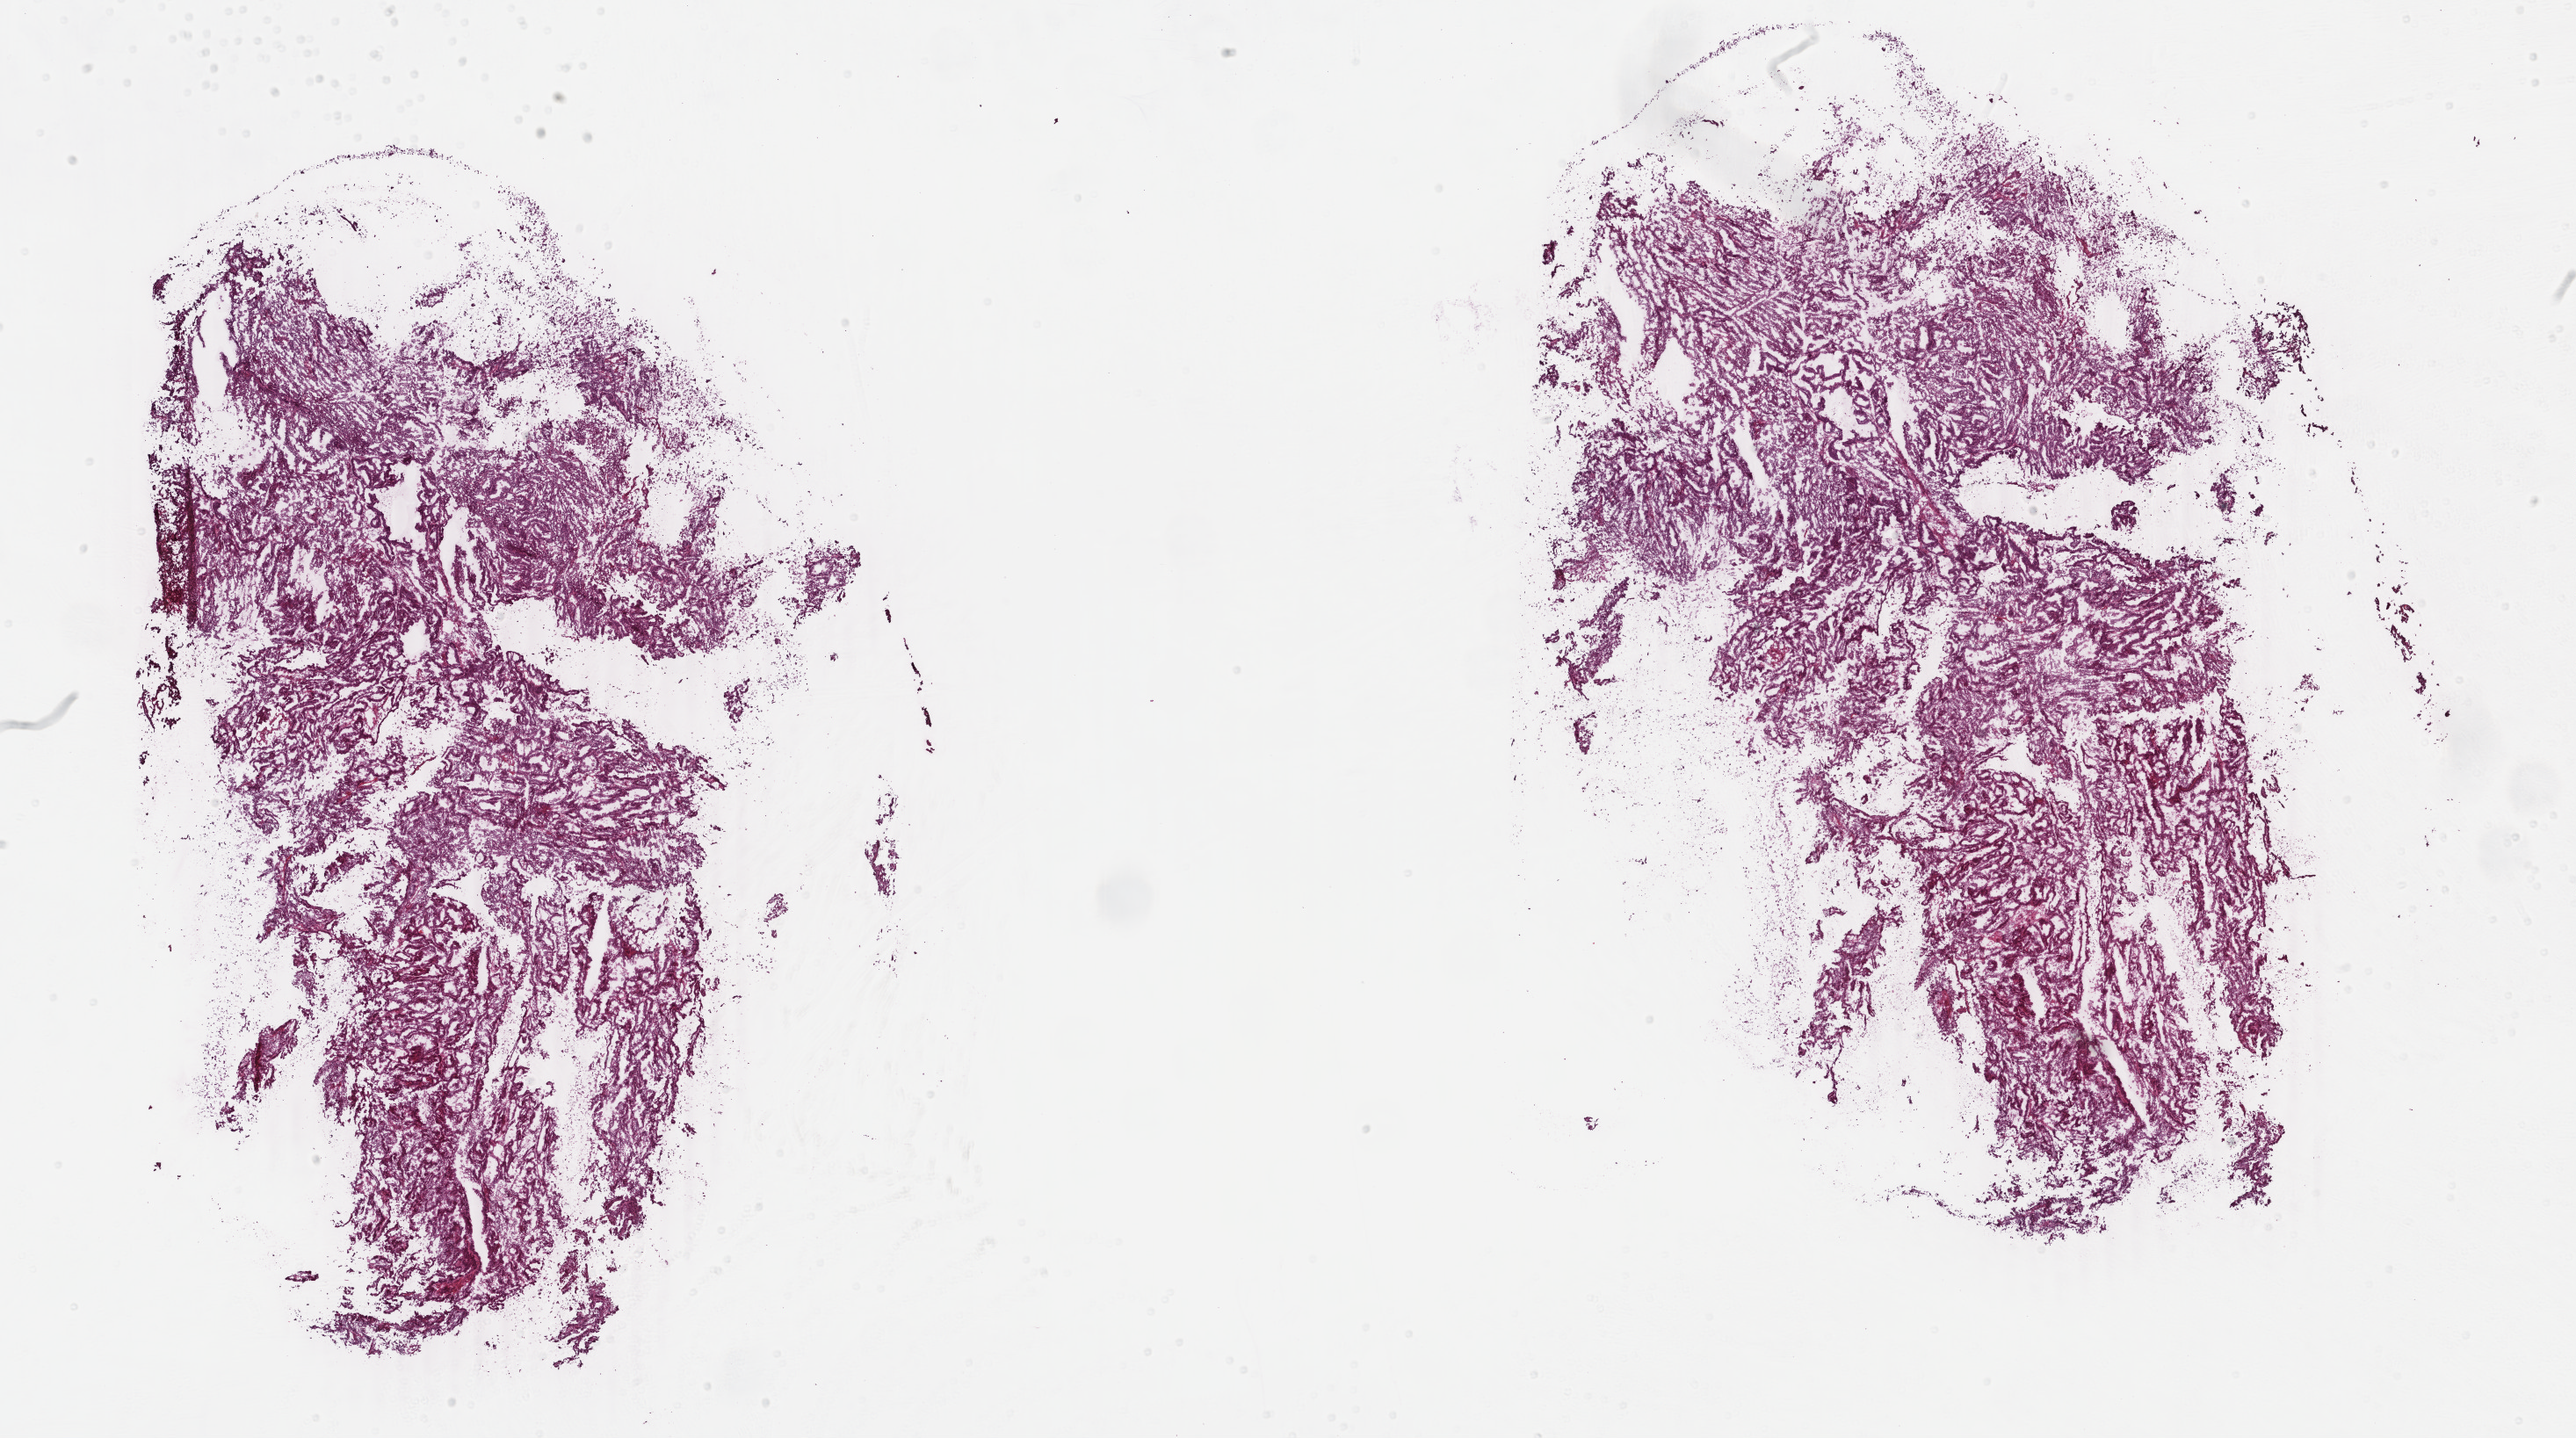
Whole-slide histology image, H&E — shown as a low-resolution overview of the whole scanned area (about 23.3 x 13.0 mm). Frozen section from the top of the tissue portion. Uterus, primary tumour sample. Female, age 82 years at initial diagnosis. Histologic grade: G1 (well differentiated). Composition of this section per pathologist review: tumour cells 83%, tumour nuclei 85%, normal cells 2%, stromal cells 5%, necrosis 10%. Inflammatory infiltration, as recorded: lymphocyte infiltration 1%, monocyte infiltration 1%, neutrophil infiltration 1%.
Histologic diagnosis: Endometrioid adenocarcinoma, NOS. FIGO stage: IB.